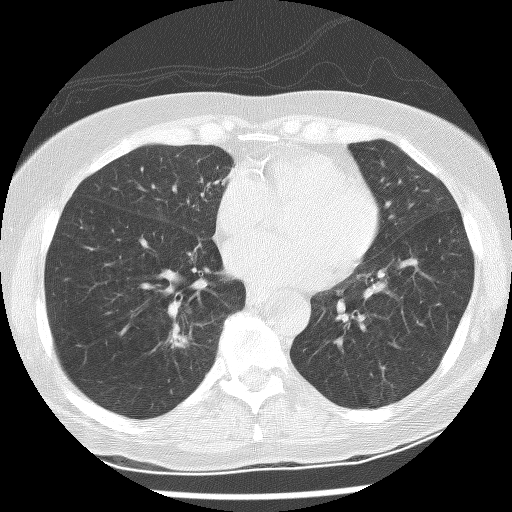
Chest CT (low-dose screening protocol), one axial image; baseline screening round; lung window (W 1500 / L -600 HU); 2.5 mm slice thickness; lung (sharp) reconstruction kernel (BONE); 120 kVp; slice 146 of 247 in the series; 512 × 512 image matrix. Female, age 60 years at enrolment.
Expert-annotated lung lesion, bounding box <156,322,204,358> (left, top, right, bottom; pixels). The exam's reader record, not a measurement of the box and not confirmed to be the same lesion: non-calcified nodule or mass ≥4 mm, right lower lobe, 10 × 6 mm, spiculated (stellate) margins, mixed attenuation. Lung cancer was diagnosed 275 days after this screen: adenocarcinoma with squamous metaplasia, right lower lobe, poorly differentiated (G3), stage IA (AJCC 6th edition), 23 mm at pathology.